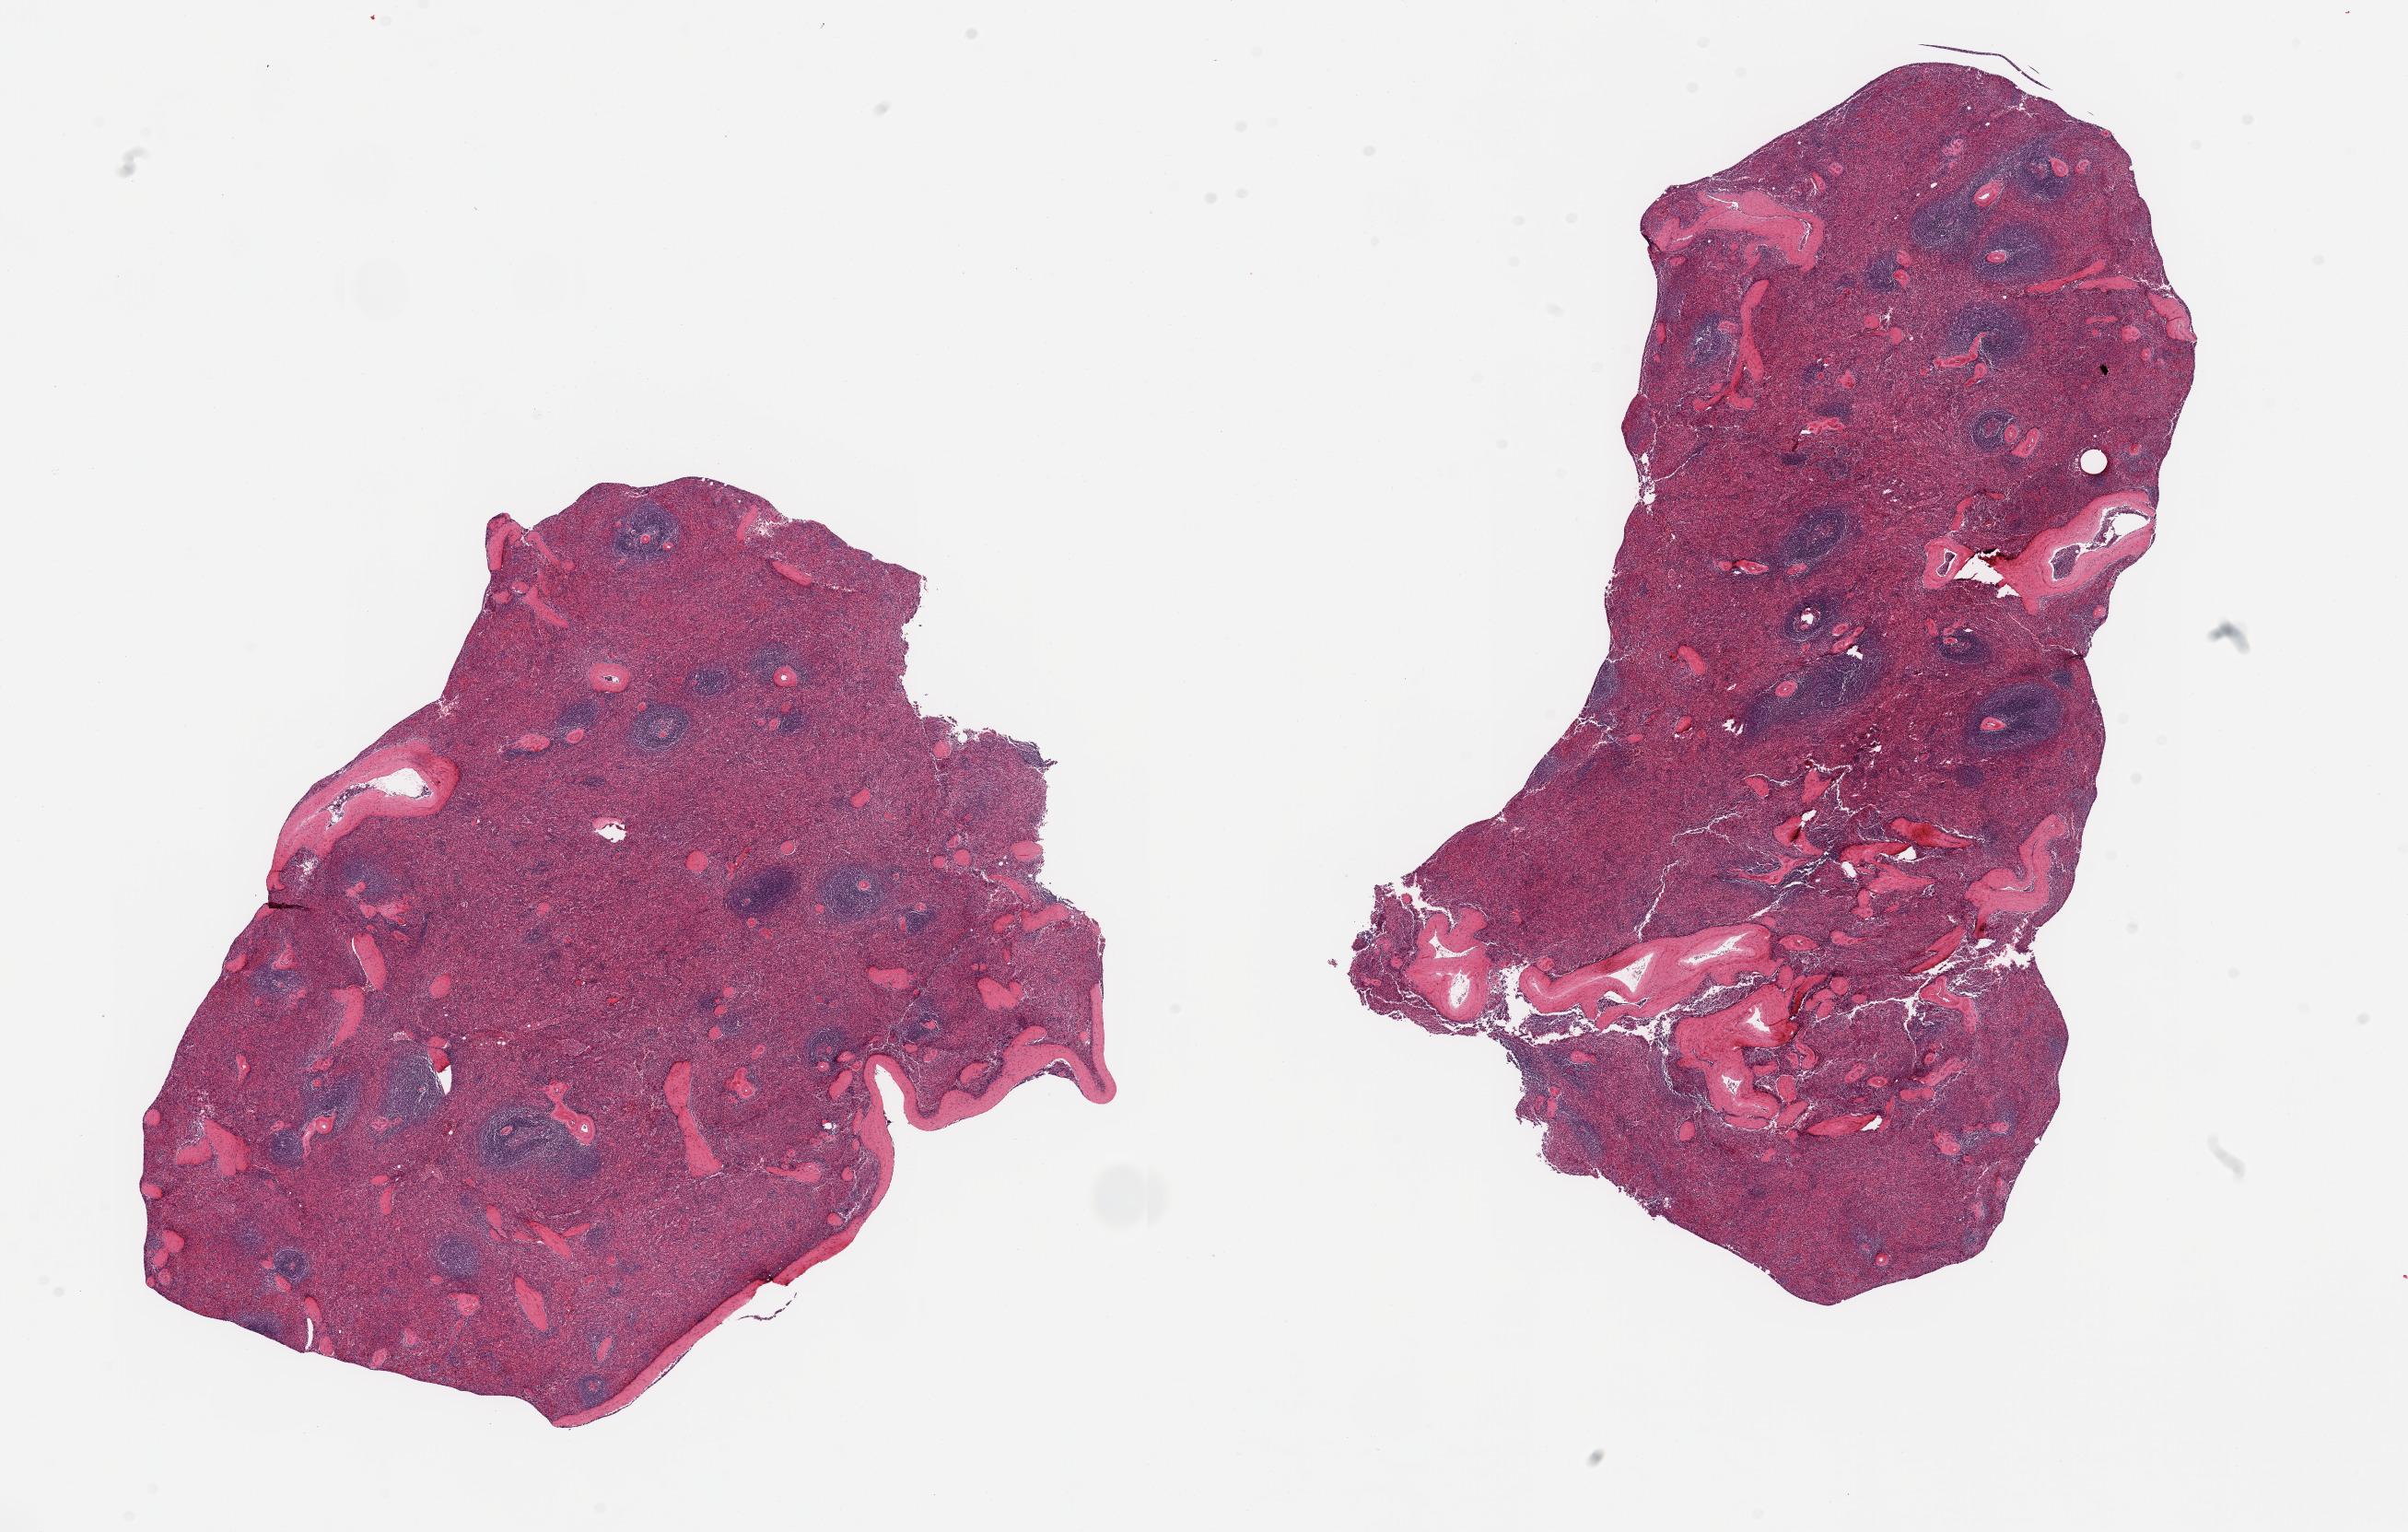
Hematoxylin and eosin (H&E) whole-slide image — a low-resolution overview of the entire scanned area, about 20.7 x 13.2 mm (acquisition: 20x scan), PAXgene-fixed paraffin-embedded (PFPE) section, target tissue: spleen, donor tissue sample. Female donor.
• review note (as recorded): 2 pieces; good lymphoid component; several large vessels